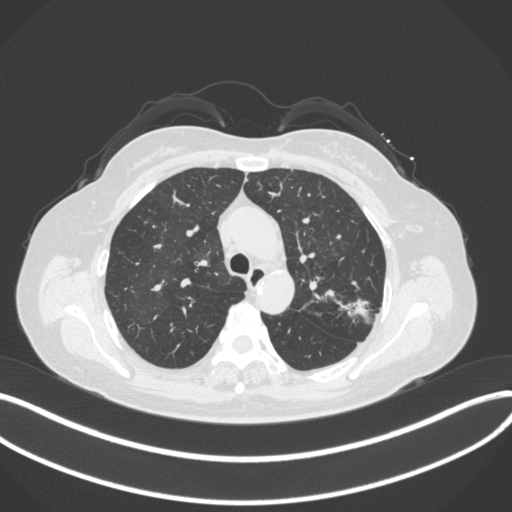
Chest CT, one axial slice; slice 244 of 330 in the series (ordered by position); reconstruction kernel B31f; 120 kVp; lung window (W 1500 / L -600 HU); 512 × 512 image matrix, field of view 400 × 400 mm. Female patient, age 60 years. From the clinical record (not read from this slice): clinical TNM (as recorded): T1c N0 M0.
Structures marked on this image (bounding box drawn by a radiologist):
- lung tumour (recorded histology: adenocarcinoma): bounding box (x1, y1, x2, y2) in pixels: (340, 291, 374, 327)